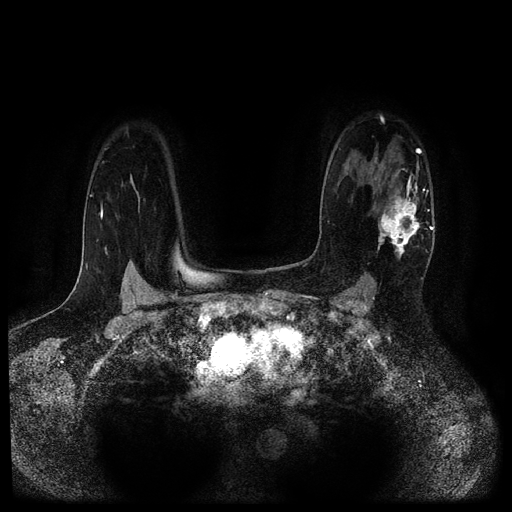
Breast MRI (dynamic contrast-enhanced, multi-phase), one axial slice. Dynamic contrast-enhanced series, time point 2 of 5 at this slice position (early post-contrast). 1.5 T. TE 2.7 ms, TR 5.4 ms. 2.2 mm slice thickness. 512 × 512 image matrix, field of view 330 × 330 mm. Patient: female, 43 years.
Outlined on this slice (semi-automatic segmentation, software-assisted and operator-edited):
- breast lesion (labelled 'tumour' in the annotation; benign lesions carry a separate 'benign' label): bounding box <375,168,430,261> (left, top, right, bottom; pixels)